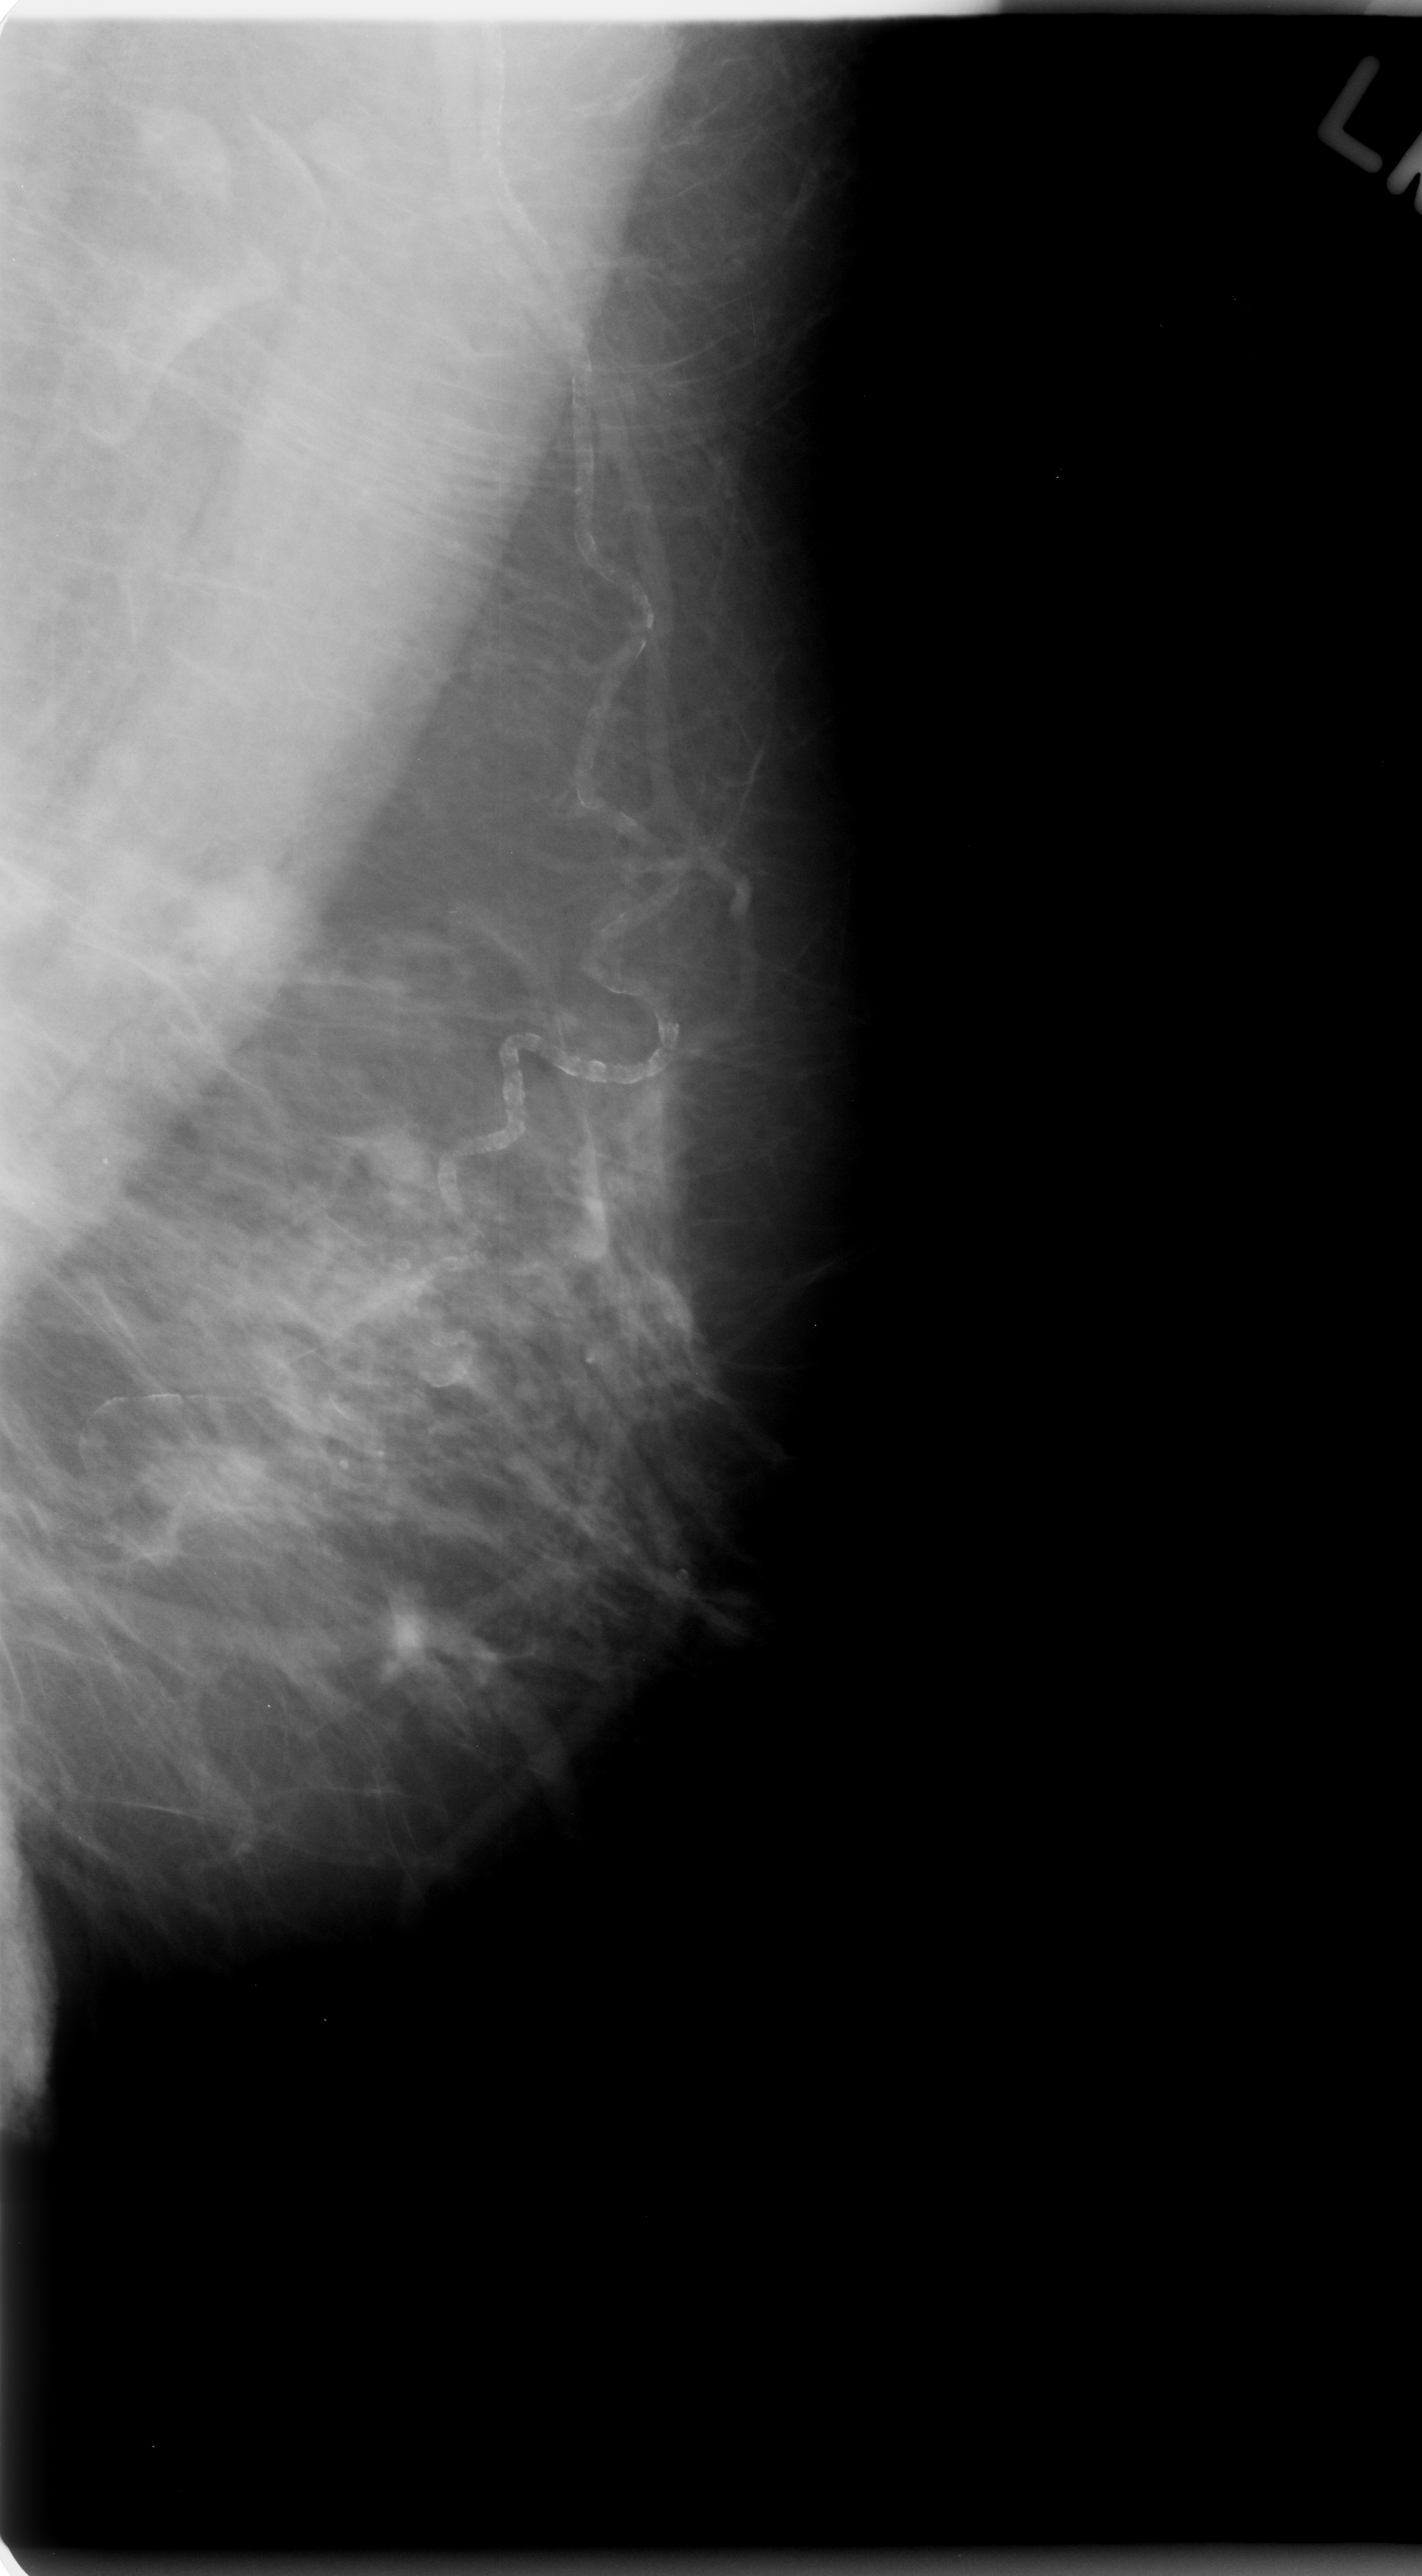
Digitized screen-film mammogram; left breast; mediolateral oblique (MLO) view; breast composition: scattered fibroglandular densities (BI-RADS density category 2 of 4); 1422 × 2576 image matrix.
Expert-marked regions of interest on this image (one box per marked abnormality):
- mass, shape lobulated, margins microlobulated; BI-RADS assessment category 4; pathology (as recorded): malignant: bounding box (x1, y1, x2, y2) in pixels: (140, 859, 321, 1031)